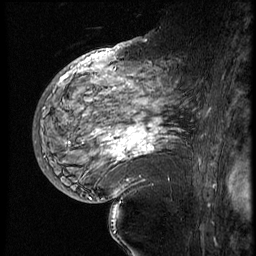
Breast MRI (dynamic contrast-enhanced), one sagittal slice. 4 images stored at this slice position (order not interpretable as contrast timing). 1.5 T. TE 4.2 ms, TR 9 ms. 2.5 mm slice thickness. 256 × 256 image matrix. Patient: female, 56 years. Case-level facts recorded for this patient, not image findings: setting: breast cancer imaged before/during neoadjuvant chemotherapy; receptor status: HER2-positive.
Structures marked on this image (semi-automatically segmented with operator editing):
- analysis volume of interest (the breast-tissue region the enhancement analysis was run in; not a lesion): bounding box <82,83,199,177> (left, top, right, bottom; pixels)
- tumour enhancement mask (voxels above the 140 % enhancement threshold inside the analysis volume of interest): <105,107,167,162>